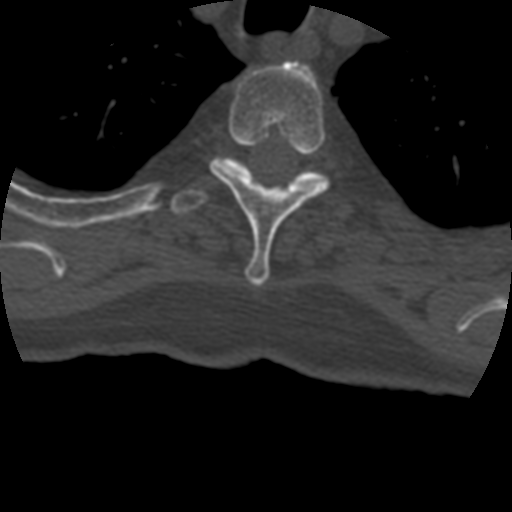
CT including the spine, one axial slice. Position 350 of 399 along the scan axis. Reconstruction kernel STANDARD. 120 kVp. Bone window (W 1800 / L 400 HU). 512 × 512 image matrix. Patient age 69 years. From the clinical record (not read from this slice): primary cancer: prostate.
Outlined on this slice (semi-automatically segmented with operator editing):
- T3 vertebra: box from (x=210, y=61) to (x=330, y=286) px
- T4 vertebra: (x=170, y=157)–(x=326, y=214)